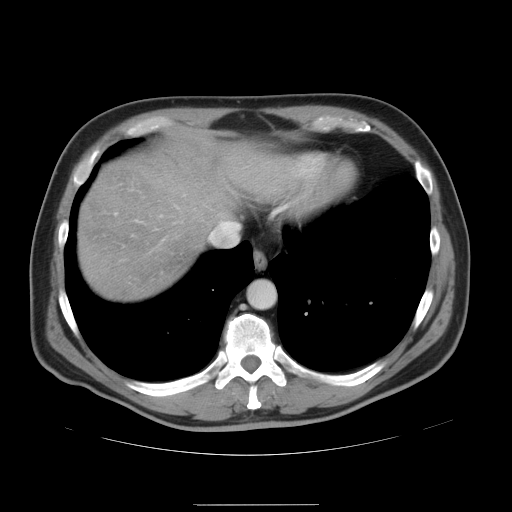
Contrast-enhanced abdominal CT, one axial slice. Position 42 of 47 along the scan axis. Intravenous contrast given. Soft-tissue window (W 400 / L 40 HU). 5 mm slice thickness. 512 × 512 image matrix, field of view 420 × 420 mm. Male patient, age 61 years. From the clinical record (not read from this slice): diagnosis: colorectal cancer liver metastases, imaged before liver resection.
Outlined on this slice (expert manual segmentation):
- hepatic veins: bounding box <209,220,239,245> (left, top, right, bottom; pixels)
- liver: <78,144,290,302>
- planned liver remnant (the part of the liver to remain after resection): <78,143,291,302>